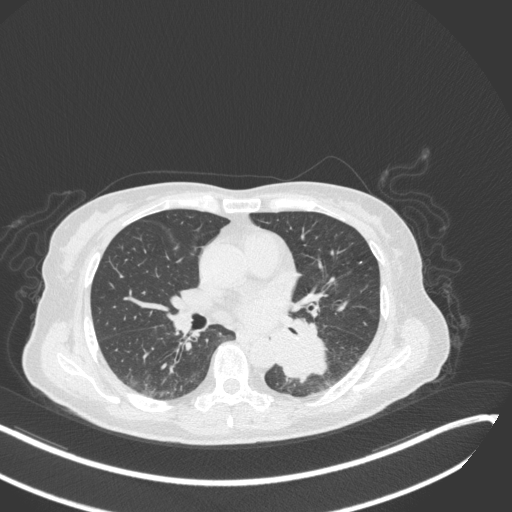
Chest CT, one axial slice; slice 141 of 342 in the series (ordered by position); reconstruction kernel B31f; 120 kVp; lung window (W 1500 / L -600 HU); 1 mm slice thickness; 512 × 512 image matrix. Female patient, age 64 years. Case-level facts recorded for this patient, not image findings: clinical TNM (as recorded): T3 N1 M1; histopathological grade: G3.
Outlined on this slice (rectangle marked by the reading radiologist):
- lung tumour (recorded histology: small cell carcinoma): bounding box (x1, y1, x2, y2) in pixels: (273, 329, 331, 391)